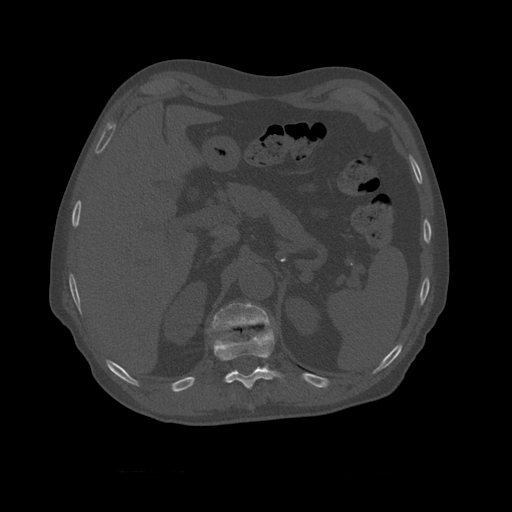
CT including the spine, one axial slice. Reconstruction kernel STANDARD. 120 kVp. Bone window (W 1800 / L 400 HU). 1.25 mm slice thickness. 512 × 512 image matrix, field of view 405 × 405 mm. Patient age 75 years. Case-level facts recorded for this patient, not image findings: primary cancer: prostate.
Structures marked on this image (semi-automatically segmented with operator editing):
- T10 vertebra: box from (x=208, y=329) to (x=287, y=390) px
- T11 vertebra: (x=210, y=302)–(x=273, y=333)